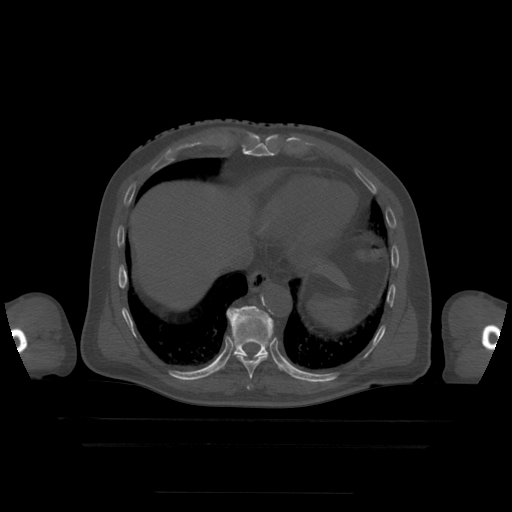
CT including the spine, one axial slice. Bone window (W 1800 / L 400 HU). 512 × 512 image matrix, field of view 436 × 436 mm. Patient age 68 years. Case-level facts recorded for this patient, not image findings: primary cancer: urothelial.
Outlined on this slice (semi-automatically segmented with operator editing):
- T10 vertebra: box from (x=227, y=306) to (x=274, y=357) px
- T9 vertebra: (x=237, y=355)–(x=269, y=390)